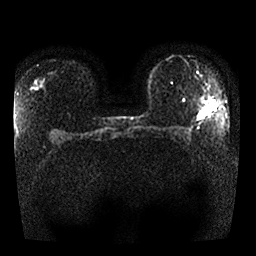
Breast MRI, one axial slice. Position 16 of 25 along the scan axis. Diffusion-weighted series; image 2 of 4 stored at this slice position (different b-values; order by instance number). 1.5 T. 4 mm slice thickness. 256 × 256 image matrix, field of view 340 × 340 mm. Female patient.
Outlined on this slice (expert manual segmentation):
- tumour on diffusion-weighted imaging: bounding box [x1, y1, x2, y2] px = [199, 105, 209, 119]